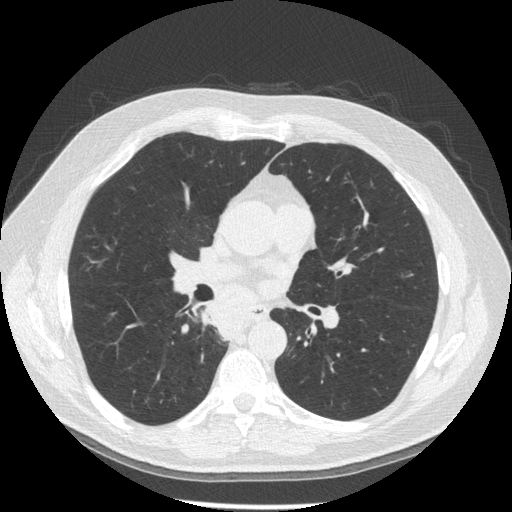
Low-dose screening chest CT, axial slice. Third screening round (two years after baseline). Lung window (W 1500 / L -600 HU). 1.25 mm slice thickness. 512 × 512 image matrix. Male, age 61 years at enrolment. Former smoker at enrolment.
- Expert-annotated lung lesion, bounding box [x1, y1, x2, y2] px = [205, 298, 256, 347].
- No non-calcified nodule or mass ≥4 mm was recorded by the screening reader at this exam.
- Official screen result: positive, other.
- Lung cancer was diagnosed 10 days after this screen: squamous cell carcinoma, keratinizing, NOS, right lower lobe, stage IIIB (AJCC 6th edition), 40 mm at pathology.